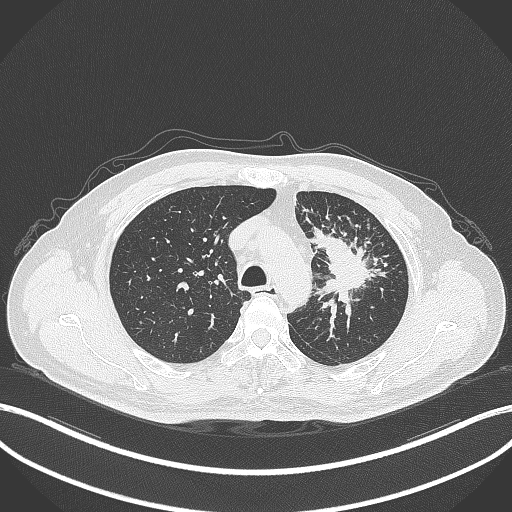
Chest CT, one axial slice. Slice 267 of 386 in the series (ordered by position). Reconstruction kernel B70f. 120 kVp. Lung window (W 1500 / L -600 HU). 1 mm slice thickness. 512 × 512 image matrix, field of view 400 × 400 mm. Patient: male, 69 years. Case-level facts recorded for this patient, not image findings: clinical TNM (as recorded): T2a N2 M0; histopathological grade: G2-3.
Structures marked on this image (bounding box drawn by a radiologist):
- lung tumour (recorded histology: adenocarcinoma): bounding box <308,225,373,301> (left, top, right, bottom; pixels)